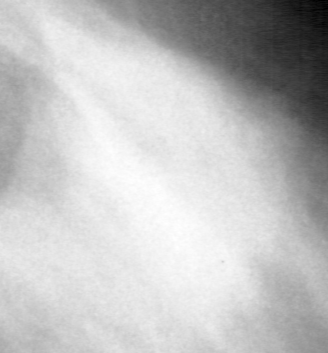
Crop from a digitized film mammogram around one marked abnormality, right breast, MLO view, BI-RADS breast density category 2 (scale 1–4).
Finding: mass, shape lobulated, margins ill defined; BI-RADS assessment category 4; subtlety rating 3 on a 1 (subtle) to 5 (obvious) scale; pathology (as recorded): benign.